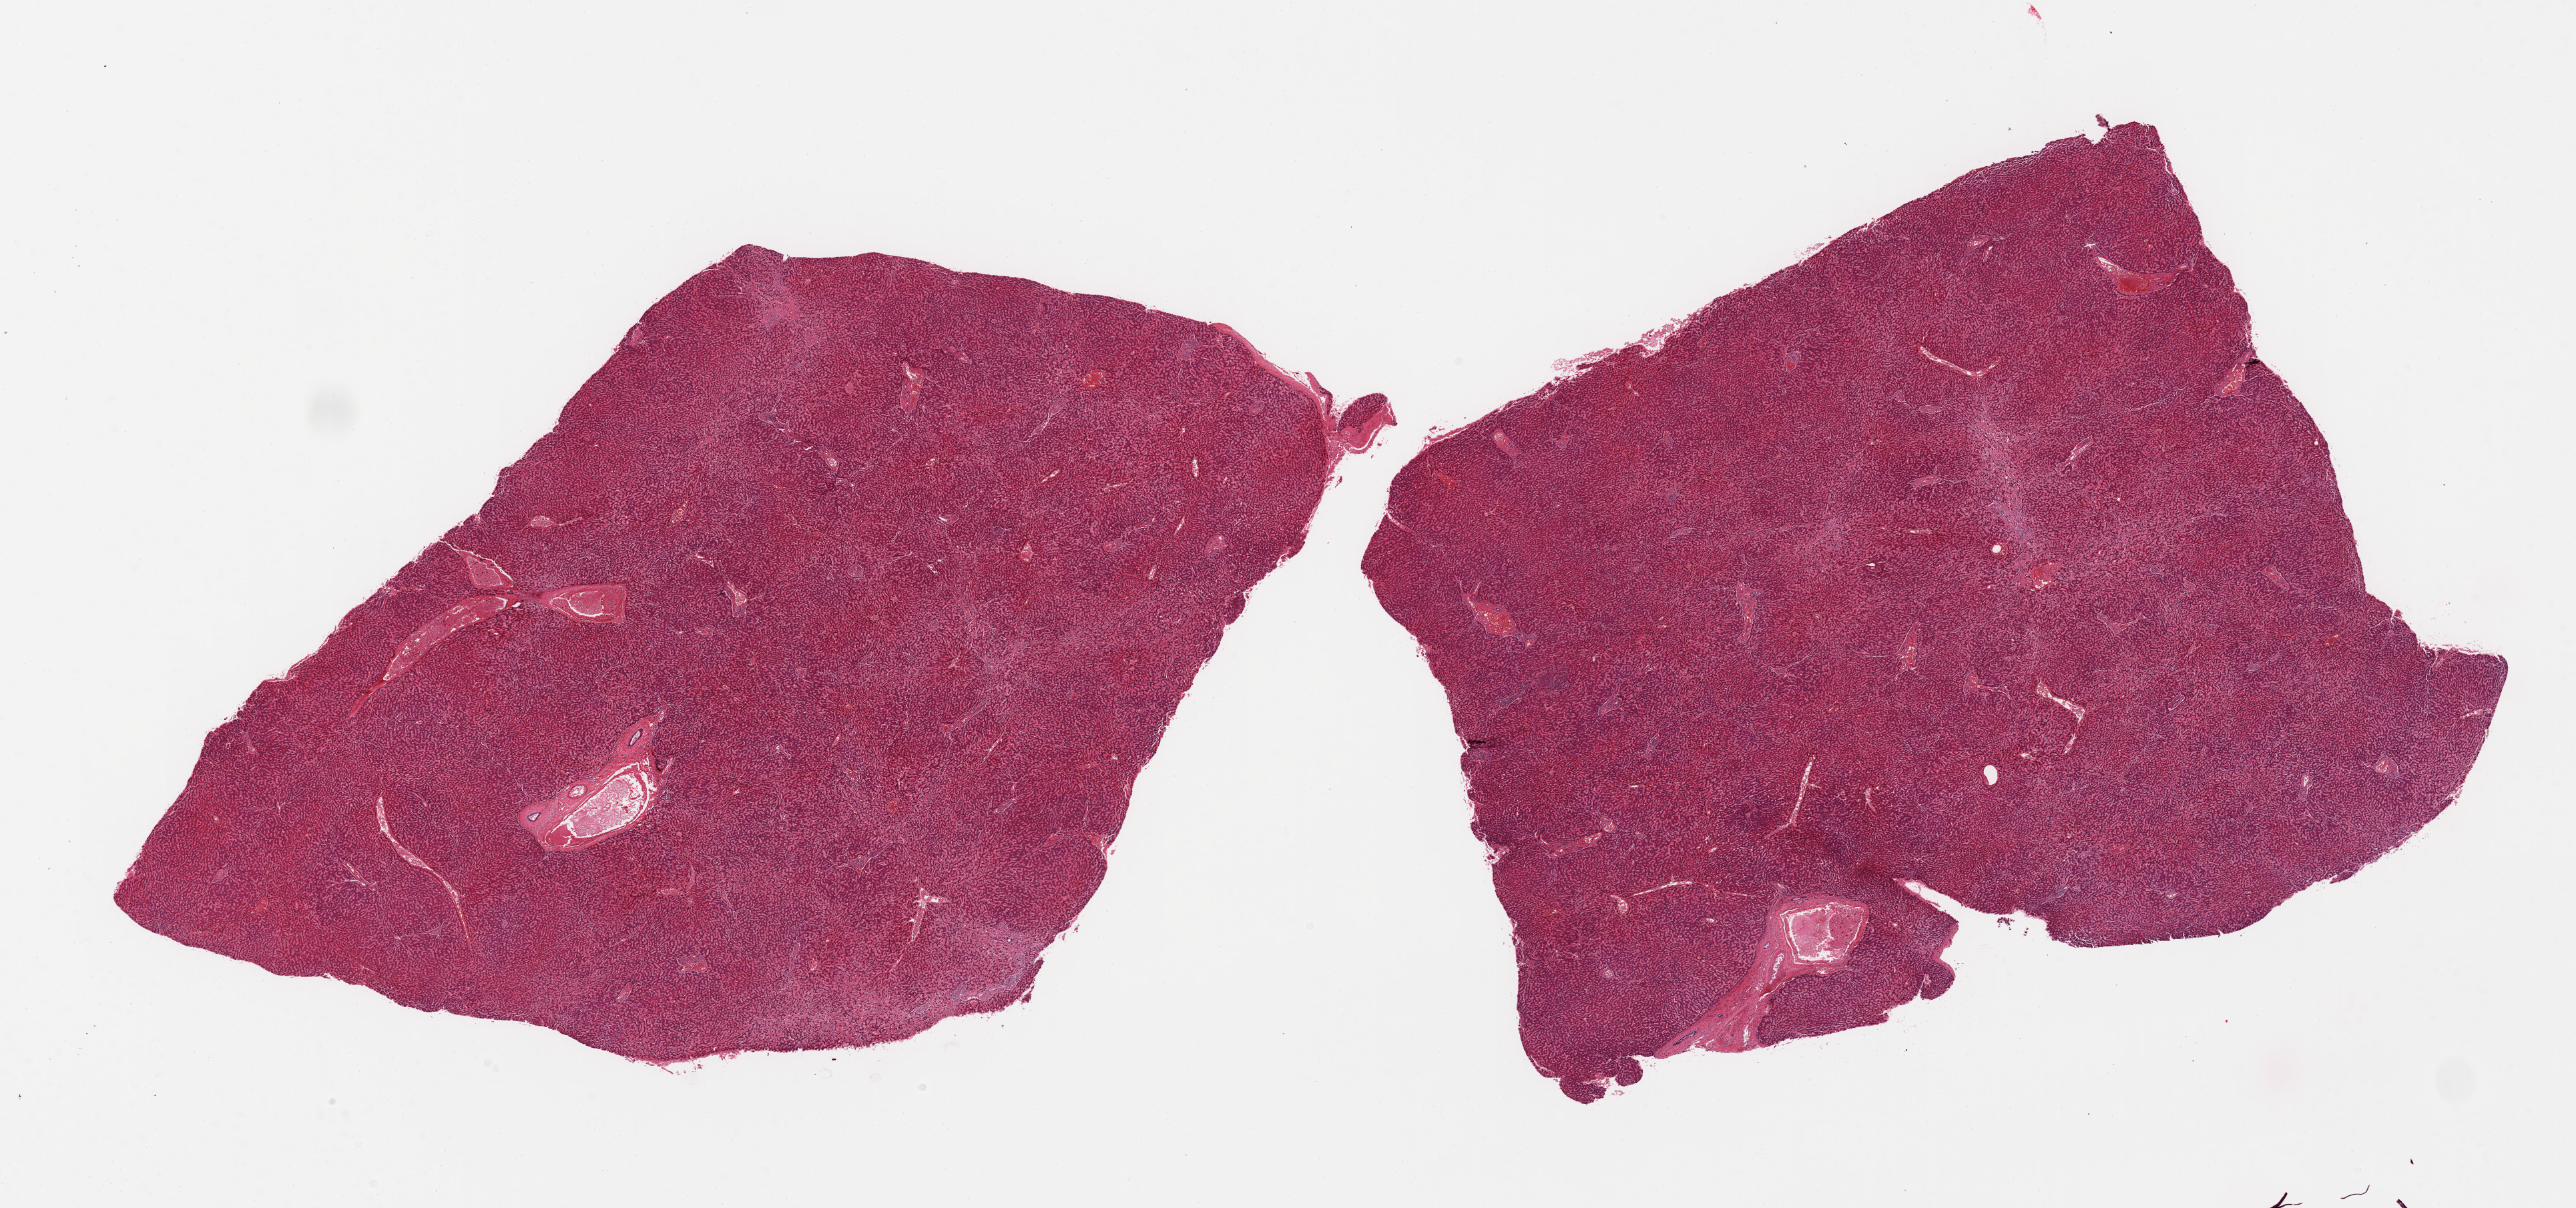
Whole-slide image, hematoxylin and eosin (H&E) stain, shown as a low-resolution overview of the whole scanned area (about 30.5 x 14.3 mm, slide scanned at 20x), PAXgene-fixed paraffin-embedded (PFPE) section, section of liver (target tissue), donor tissue sample. Donor: male.
Reviewer comment on this tissue sample: 2 pieces, moderate fibrosis/cardiac cirrhosis pattern.